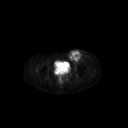
FDG PET of an extremity soft-tissue mass (from a PET/CT study), one axial slice. Slice 71 of 267 in the series (ordered by position). 3.27 mm slice thickness. 128 × 128 image matrix, field of view 600 × 600 mm. Female patient, age 24 years. Case-level facts recorded for this patient, not image findings: histological type: leiomyosarcoma; grade: high; site of the primary tumour: groin.
Outlined on this slice (expert contour drawn on MRI and transferred to this co-registered scan by the dataset authors):
- gross tumour volume including surrounding oedema: bounding box [x1, y1, x2, y2] px = [67, 49, 91, 66]
- gross tumour volume (mass): [67, 50, 83, 63]